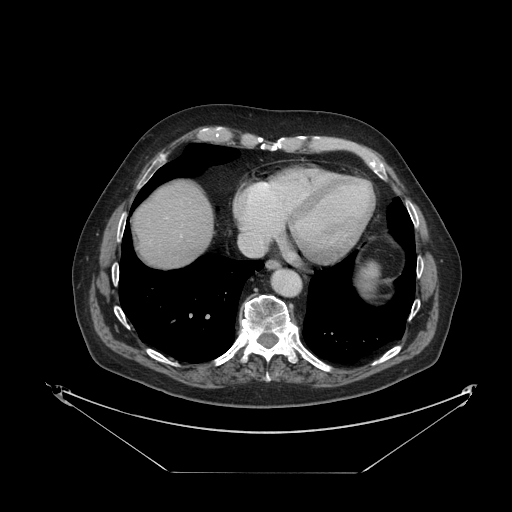
Contrast-enhanced abdominal CT, one axial slice. Slice 114 of 121 in the series (ordered by position). 120 kVp. Intravenous contrast given. Soft-tissue window (W 400 / L 40 HU). 2.5 mm slice thickness. 512 × 512 image matrix, field of view 500 × 500 mm. Male patient, age 68 years. Case-level facts recorded for this patient, not image findings: diagnosis: colorectal cancer liver metastases, imaged before liver resection; multiple liver metastases: no; largest metastasis: 4 cm.
Structures marked on this image (expert manual segmentation):
- liver: box from (x=135, y=182) to (x=213, y=268) px
- planned liver remnant (the part of the liver to remain after resection): (x=135, y=182)–(x=213, y=268)